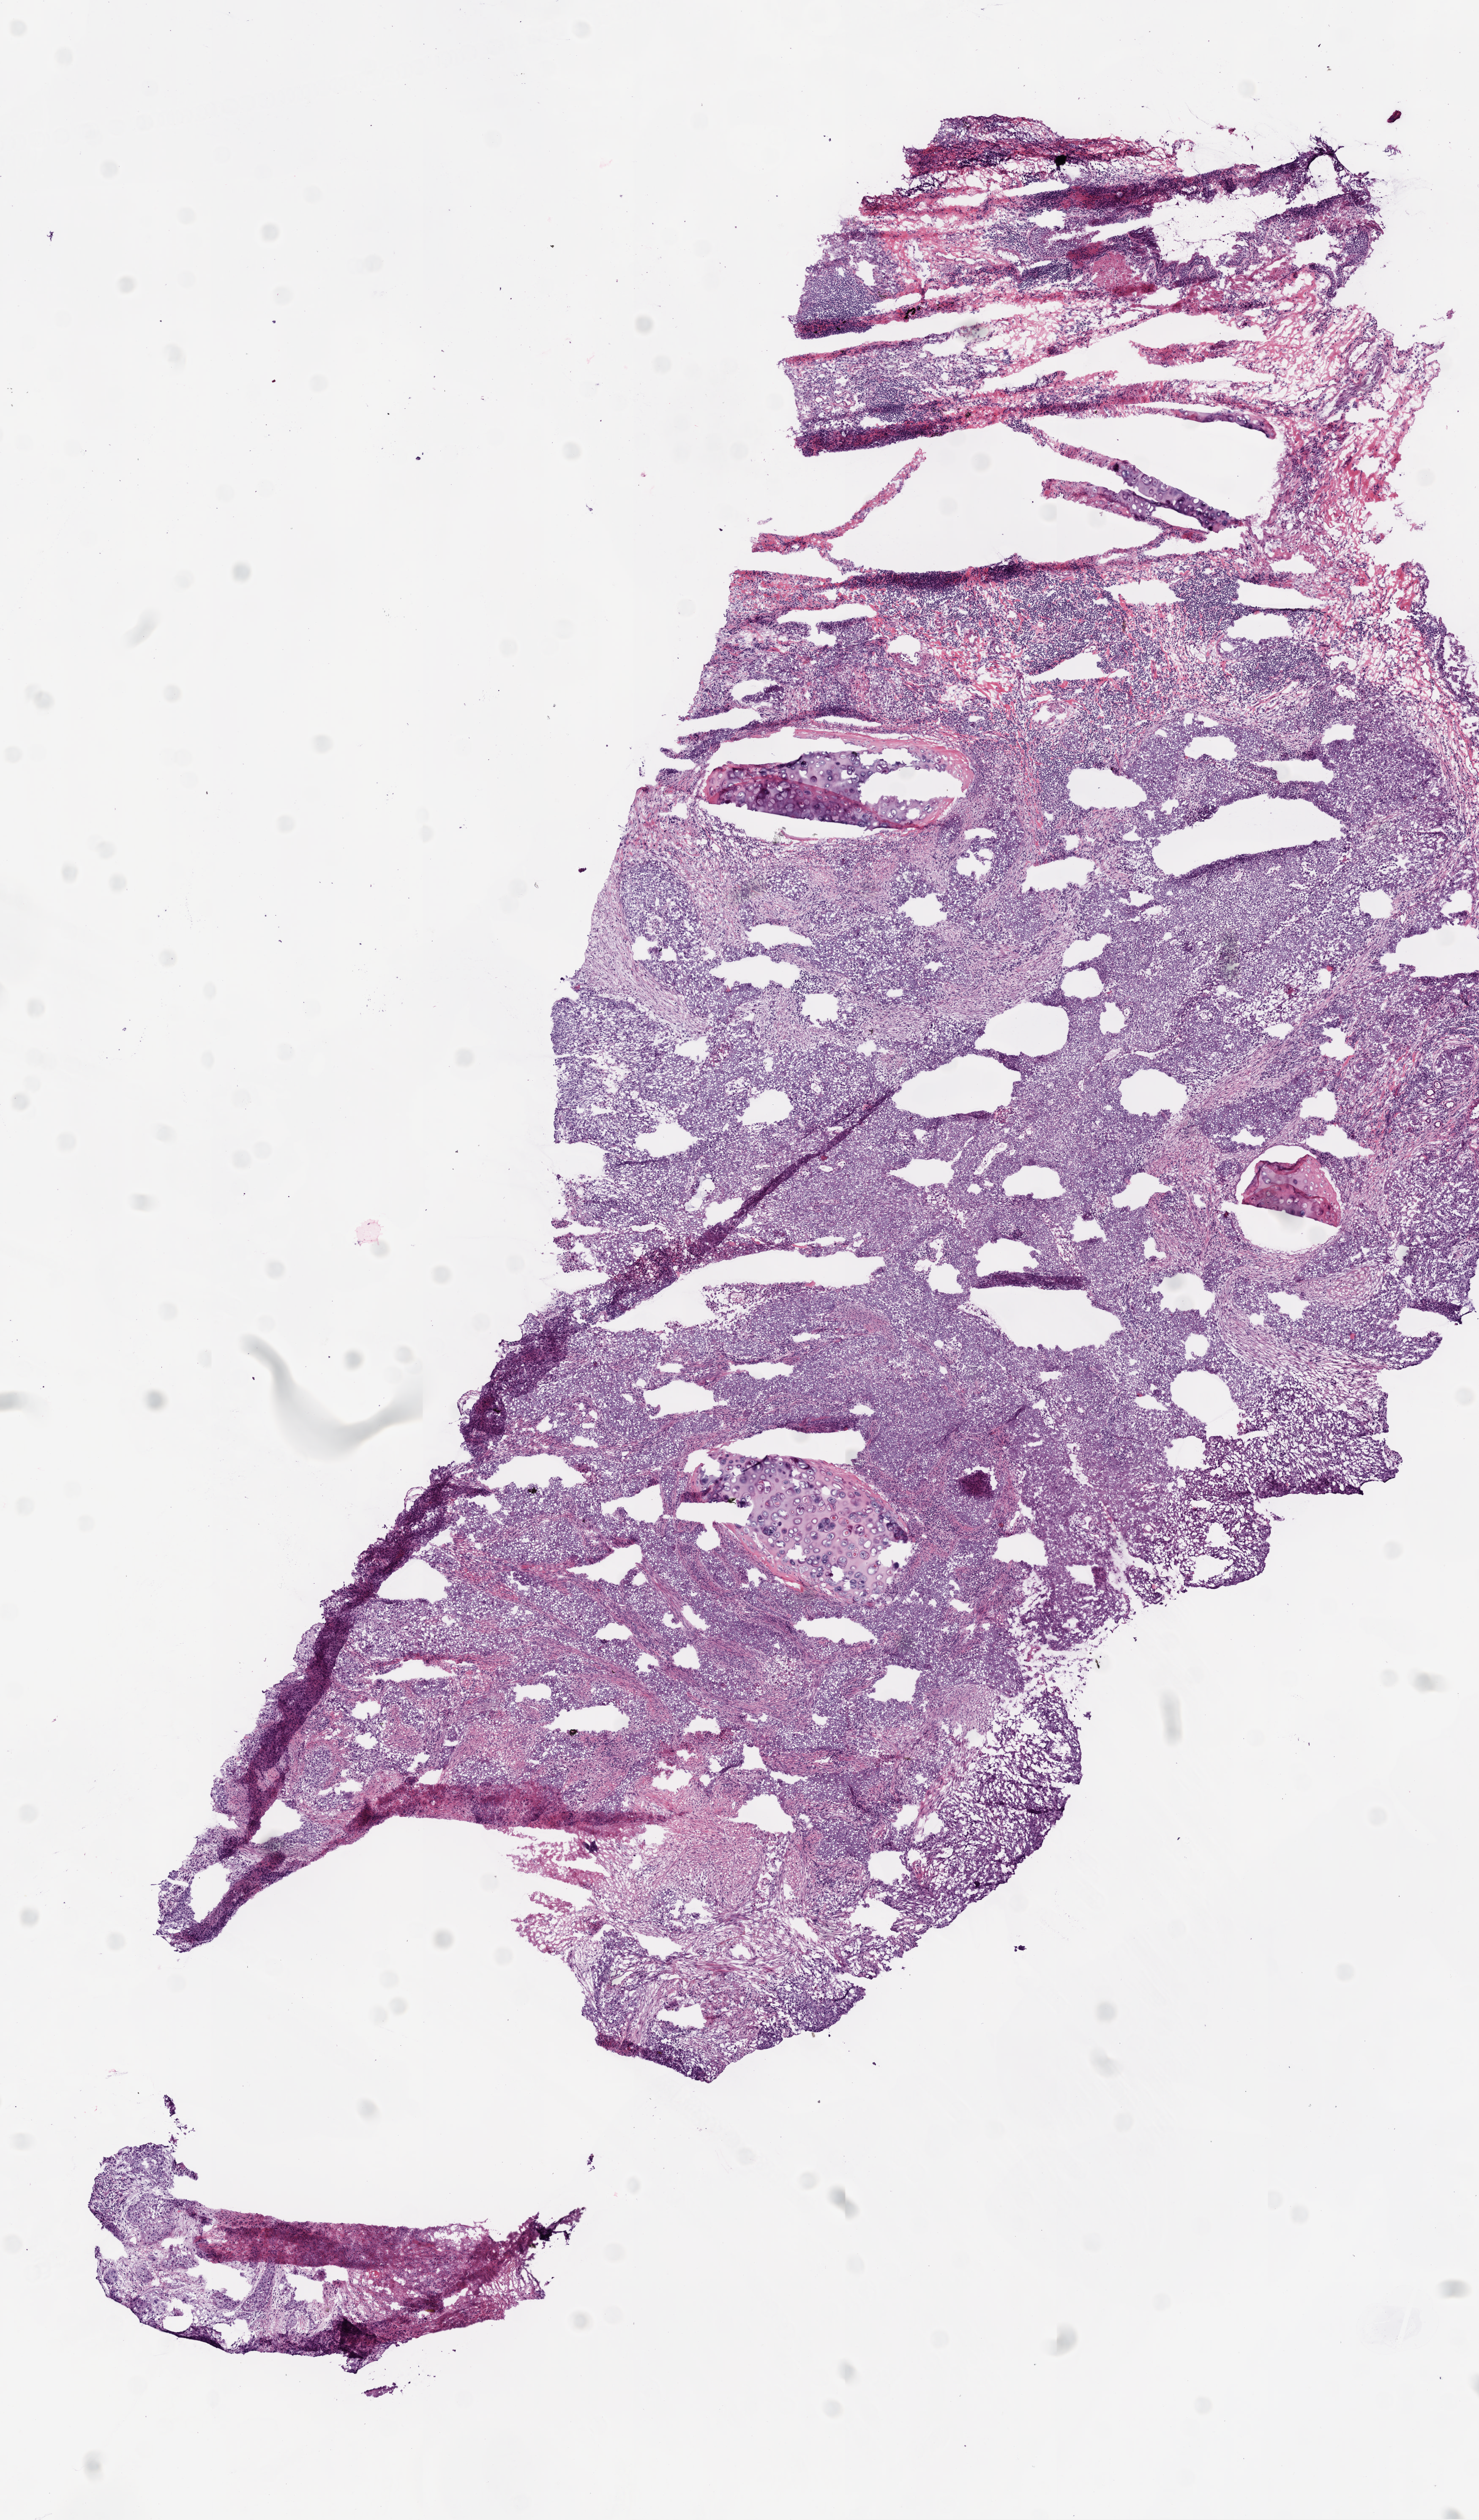
Digitized Hematoxylin and eosin (H&E) stained tissue section (whole slide) — a low-resolution overview of the entire scanned area, about 7.0 x 12.0 mm (slide scanned at 20x). Frozen section. Lung, primary tumour sample. Male, age 72 years at initial diagnosis. Composition of this section per pathologist review: tumour cells 70%, tumour nuclei 70%, normal cells 15%, stromal cells 10%, necrosis 5%.
- histologic diagnosis: Squamous cell carcinoma, NOS (upper lobe, lung)
- TNM: T2 N1 M0
- AJCC pathologic stage: IIB (6th edition)